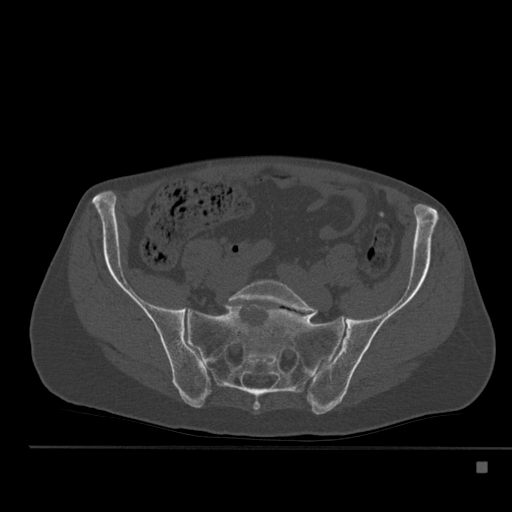
CT including the spine, one axial slice; slice 104 of 517 in the series (ordered by position); bone window (W 1800 / L 400 HU); 1.5 mm slice thickness; 512 × 512 image matrix, field of view 408 × 408 mm. Patient: male, 70 years. Case-level facts recorded for this patient, not image findings: primary cancer: renal; vertebrae with lytic lesions (as recorded): T4, T6, T10, T12, L3, L4, L5.
Annotated regions visible in this slice (semi-automatic segmentation, software-assisted and operator-edited):
- L5 vertebra: box from (x=228, y=280) to (x=317, y=315) px